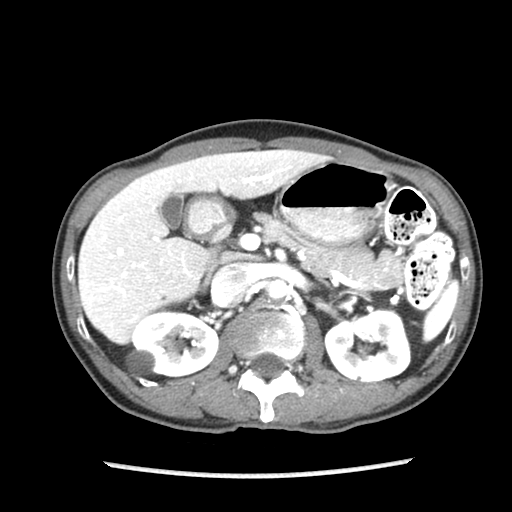
Contrast-enhanced abdominal CT (liver protocol), one axial slice; slice 48 of 87 in the series (ordered by position); soft-tissue window (W 400 / L 40 HU); 512 × 512 image matrix, field of view 300 × 300 mm. From the clinical record (not read from this slice): diagnosis: hepatocellular carcinoma (patient treated with transarterial chemoembolisation; whether this scan precedes or follows treatment is not stated here); TNM stage (as recorded): Stage-IIIB.
Outlined on this slice (semi-automatically segmented with operator editing):
- liver parenchyma outside the tumour (the mass and vessels are separate outlines, so this box may not span the whole liver): bounding box <78,150,329,342> (left, top, right, bottom; pixels)
- liver vessels: <89,166,290,320>